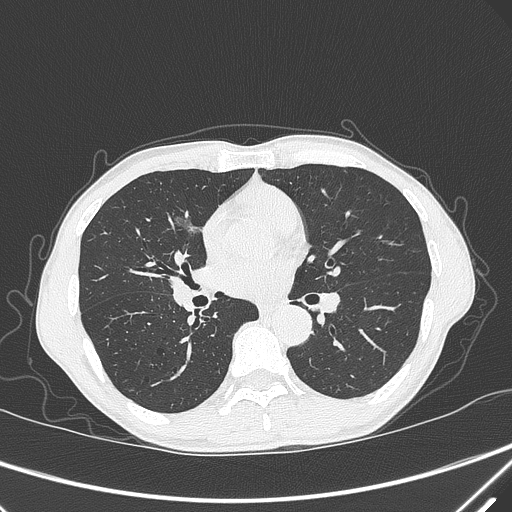
Chest CT, one axial slice; position 173 of 339 along the scan axis; 120 kVp; lung window (W 1500 / L -600 HU); 1 mm slice thickness; 512 × 512 image matrix. Male patient, age 67 years. Case-level facts recorded for this patient, not image findings: clinical TNM (as recorded): T1c N0 M0; histopathological grade: G1-2.
Structures marked on this image (rectangle marked by the reading radiologist):
- lung tumour (recorded histology: adenocarcinoma): bounding box <170,206,206,246> (left, top, right, bottom; pixels)